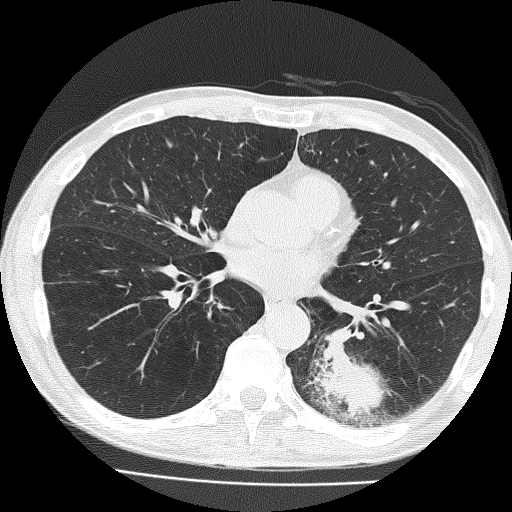
Chest CT (low-dose screening protocol), one axial image. Baseline screening round. Lung window (W 1500 / L -600 HU). Slice 85 of 160 in the series. 512 × 512 image matrix, field of view 324 × 324 mm. Male, age 58 years at enrolment. Current smoker at enrolment.
Lesion marked by an expert reader, bounding box (x1, y1, x2, y2) in pixels: (303, 314, 419, 434). The screening reader recorded 2 non-calcified nodules or masses ≥4 mm on this exam (left lower lobe, left upper lobe); which of them this box marks is not recorded. Participant outcome: lung cancer diagnosed 39 days after this screen — non-small cell carcinoma, left lower lobe, poorly differentiated (G3), stage IV (AJCC 6th edition), 74 mm at pathology.